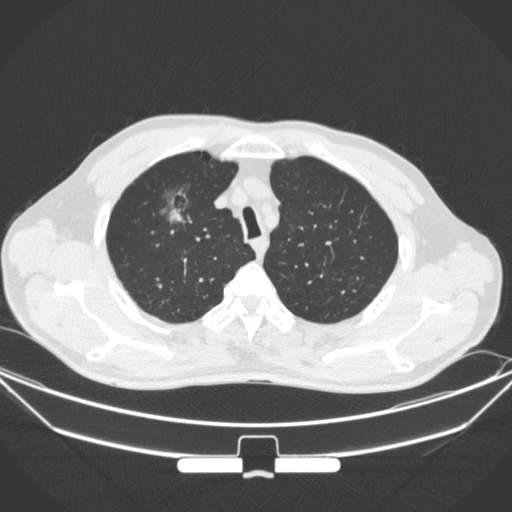
Chest CT, one axial slice. Position 282 of 355 along the scan axis. 120 kVp. Lung window (W 1500 / L -600 HU). 1 mm slice thickness. 512 × 512 image matrix, field of view 399 × 399 mm. Male patient, age 67 years. From the clinical record (not read from this slice): clinical TNM (as recorded): T1c N0 M0.
Outlined on this slice (rectangle marked by the reading radiologist):
- lung tumour (recorded histology: adenocarcinoma): bounding box <158,175,195,229> (left, top, right, bottom; pixels)